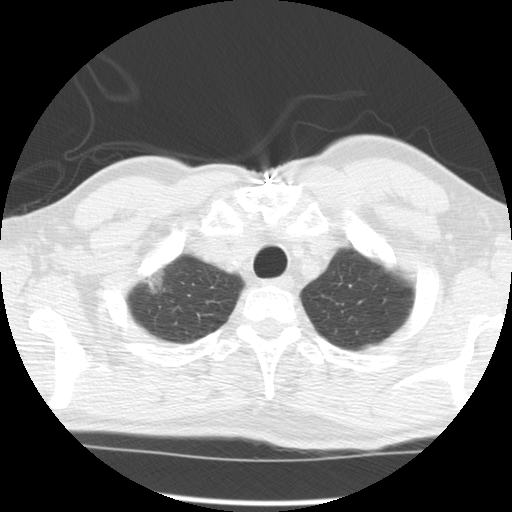
Chest CT (low-dose screening protocol), one axial image; second annual screen; lung window (W 1500 / L -600 HU); 2.5 mm slice thickness. Male, age 64 years at enrolment. Former smoker at enrolment.
Expert reader's lesion annotation, bounding box (x1, y1, x2, y2) in pixels: (122, 246, 178, 312). The screening reader recorded 2 non-calcified nodules or masses ≥4 mm on this exam (right upper lobe, left upper lobe); which of them this box marks is not recorded. Lung cancer was diagnosed 429 days after this screen (after the third annual screen): adenocarcinoma, NOS, right upper lobe, well differentiated (G1), stage IB (AJCC 6th edition), 45 mm at pathology.